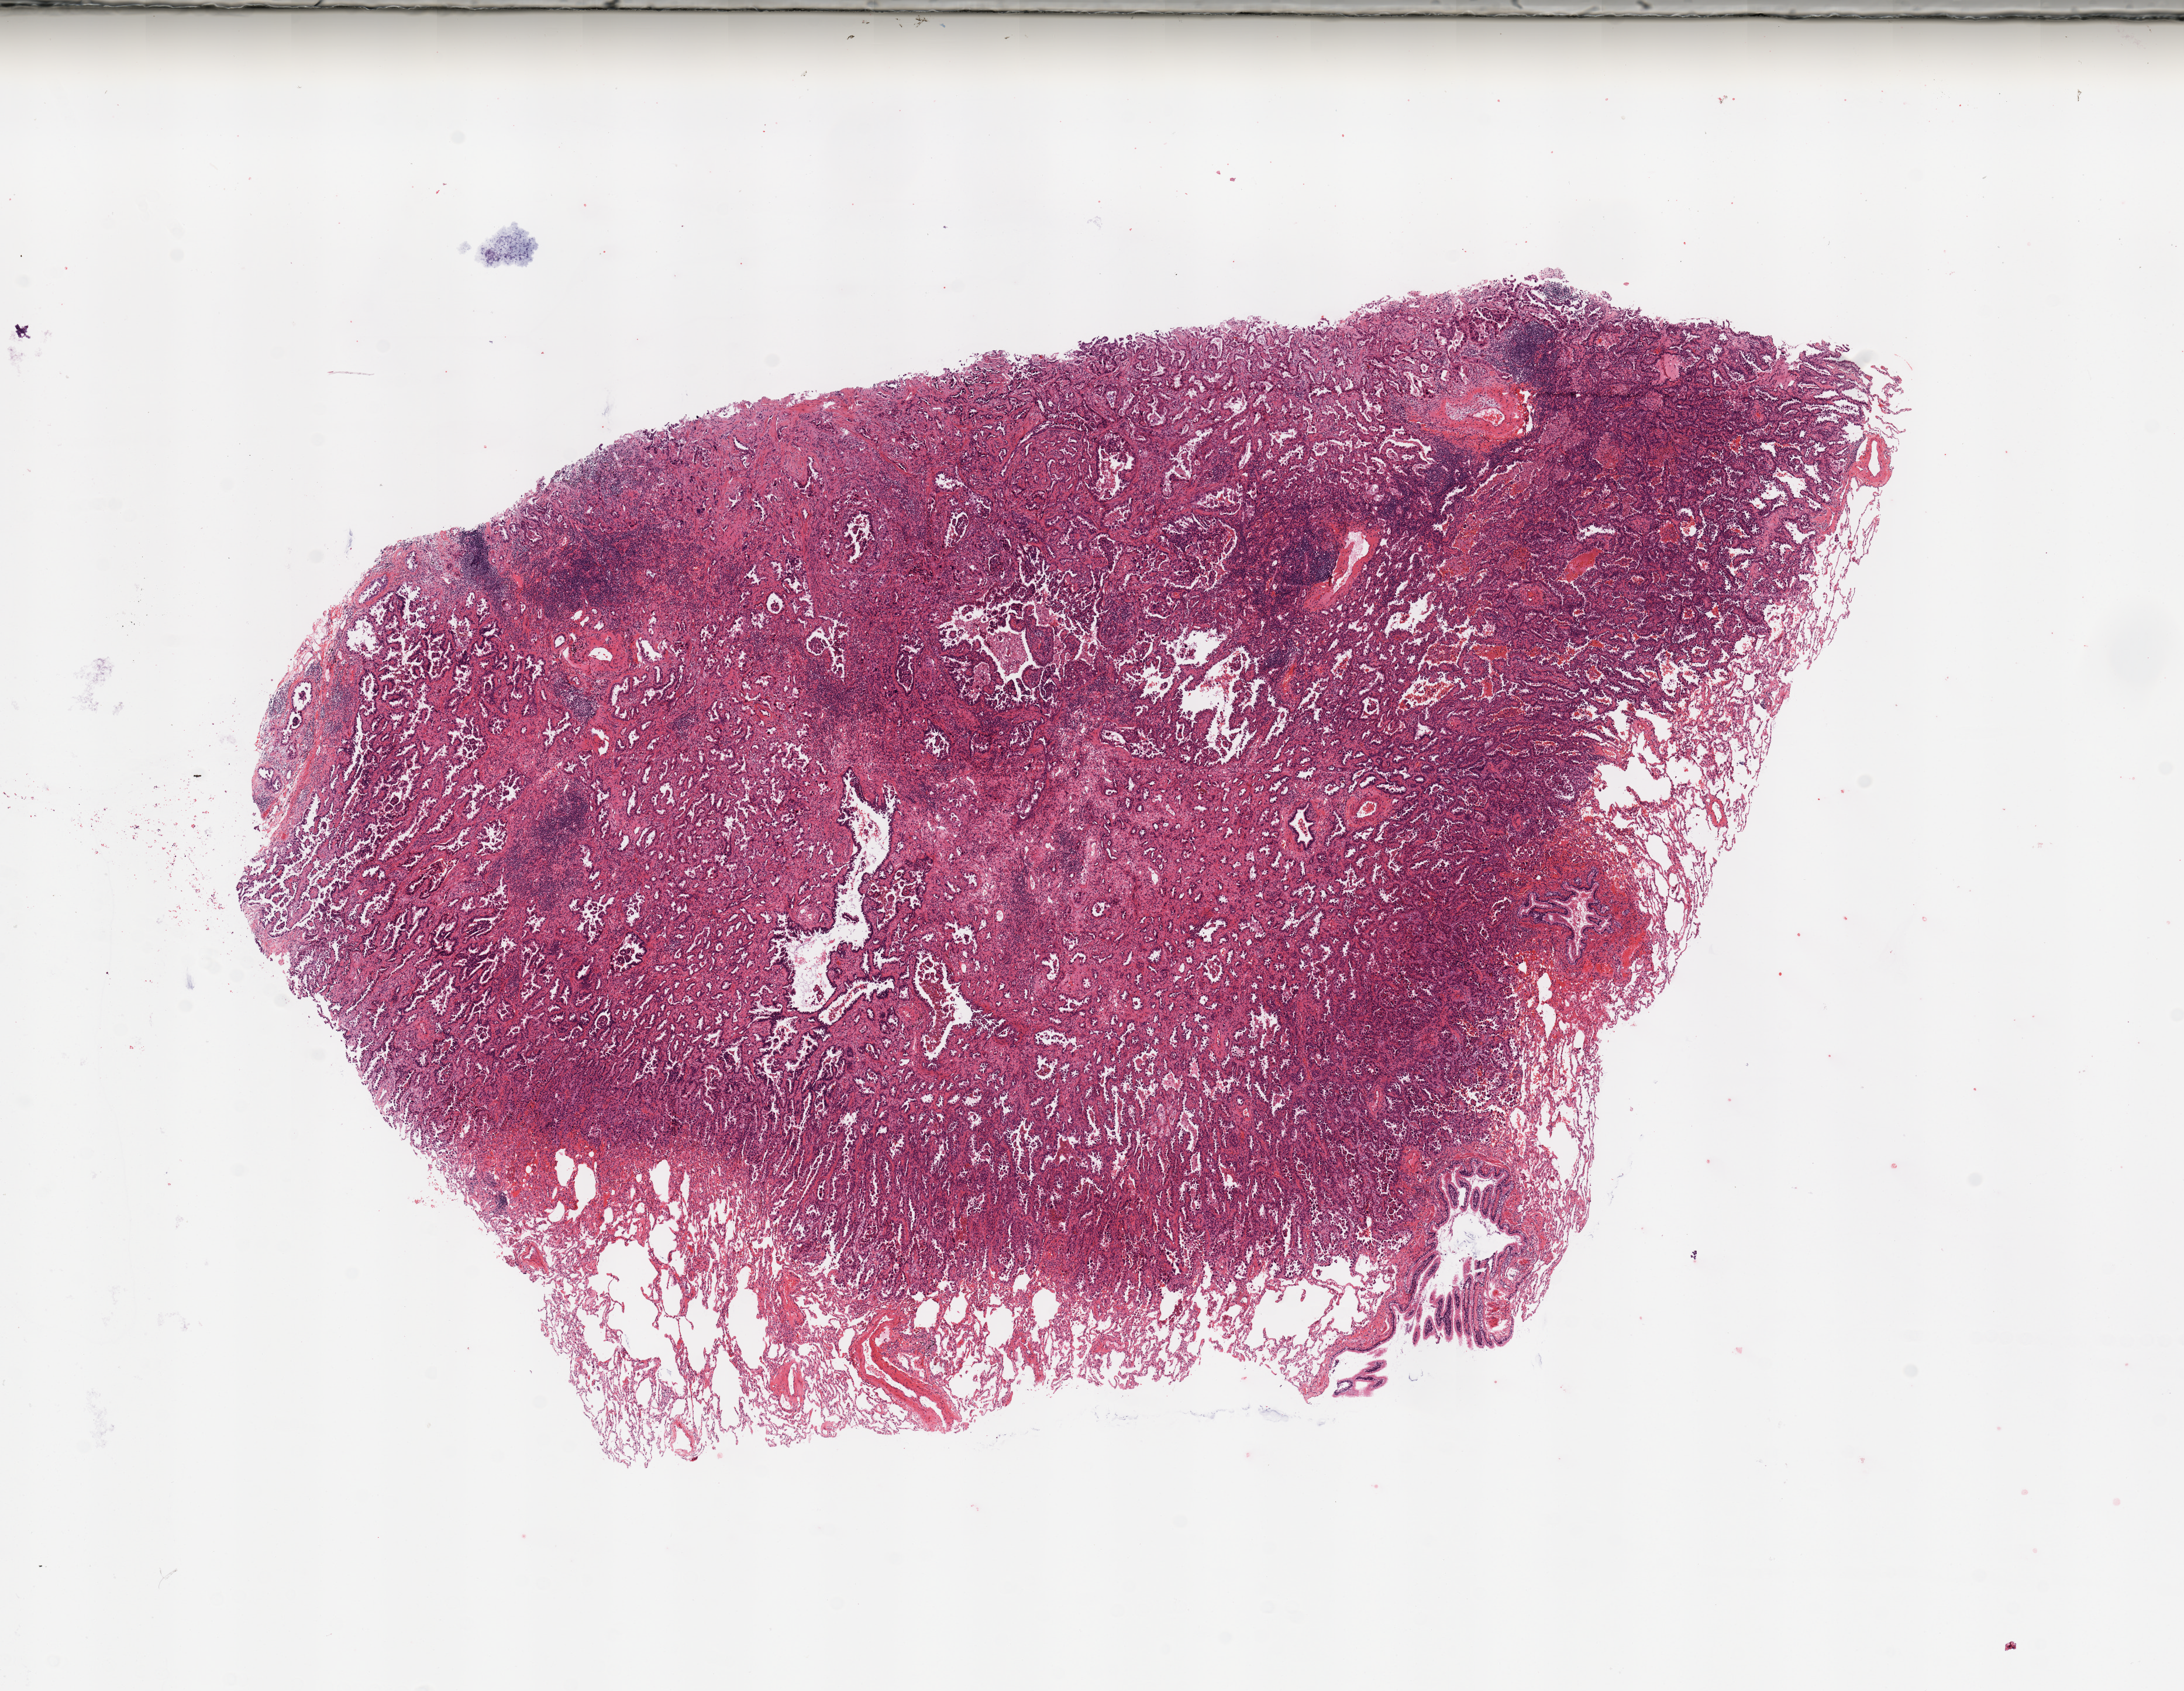
Whole-slide histology image, H&E-stained, shown as a low-resolution overview of the whole scanned area (about 14.8 x 11.4 mm, acquisition: 20x scan); tumour tissue sample, sampled site: lung. Patient: female, age 46 years. Composition of this section per pathologist review: tumour nuclei 75%, necrosis 0%.
Diagnosis: Adenocarcinoma, NOS.